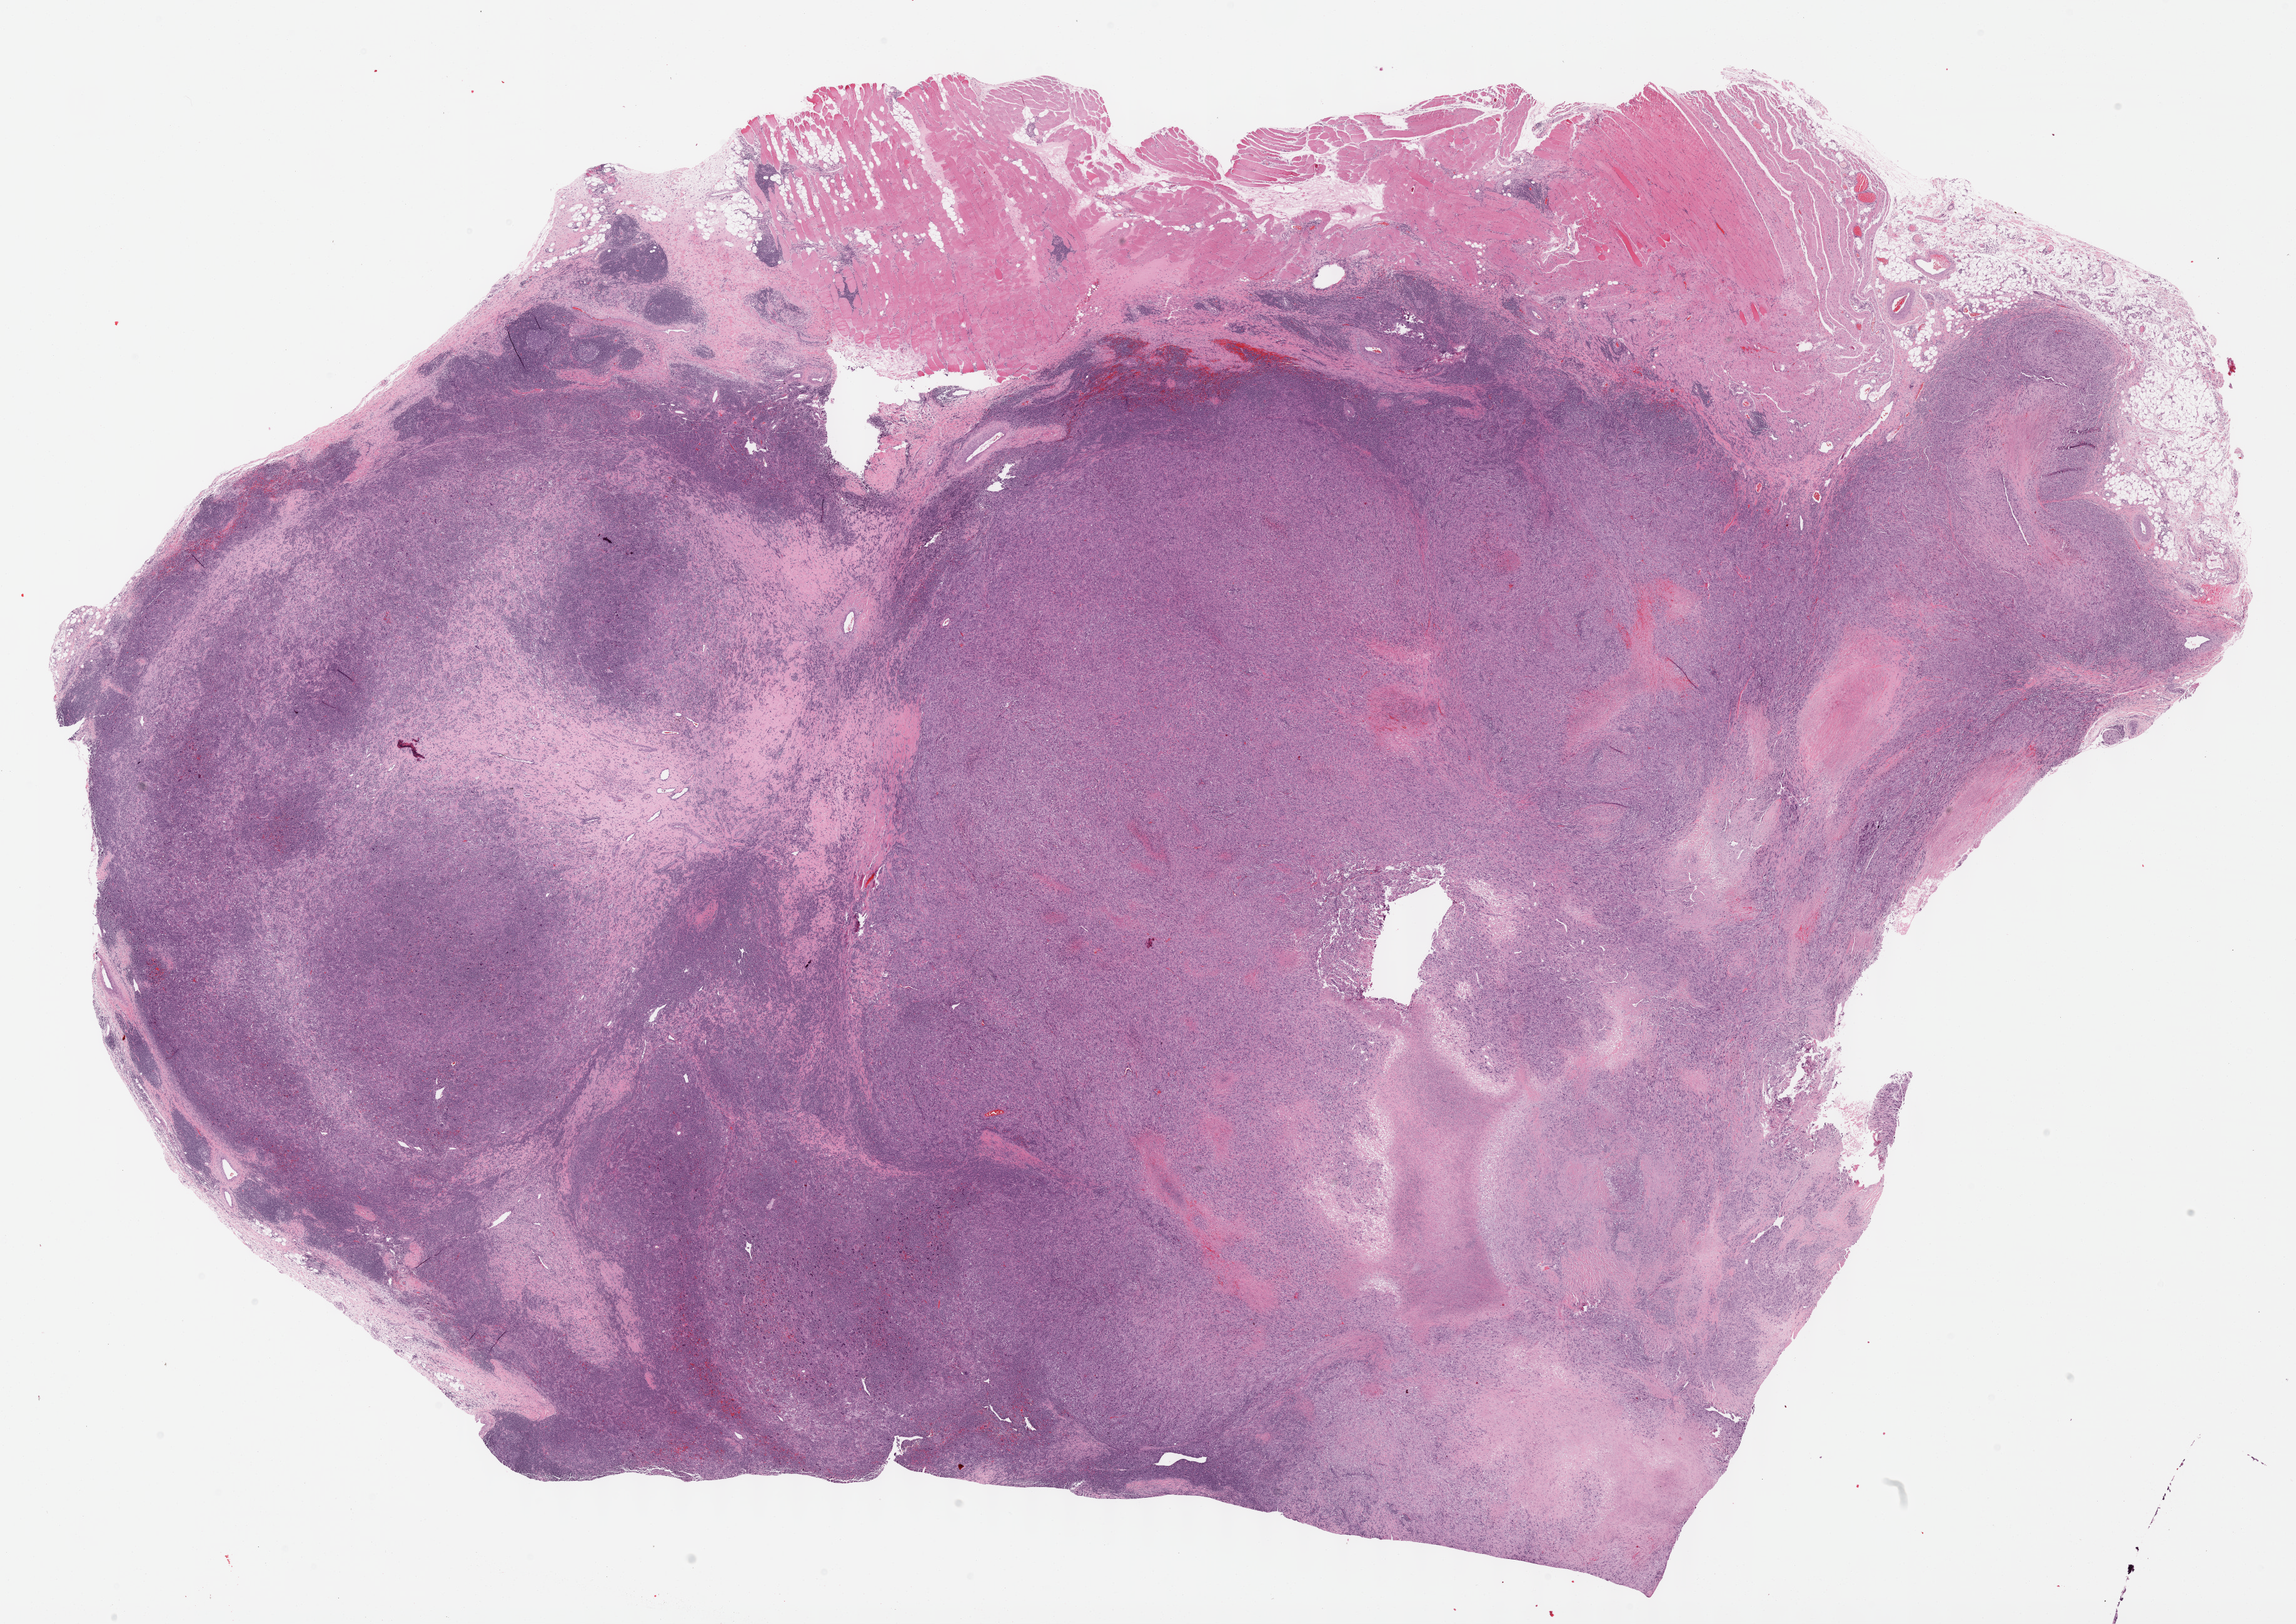
H&E whole-slide image, whole scanned area (about 29.7 x 21.0 mm, acquisition: 40x scan) shown as a low-resolution overview, formalin-fixed paraffin-embedded (FFPE) diagnostic section, primary tumour sample from the connective, subcutaneous and other soft tissues. Patient: male, age at initial diagnosis 59 years.
Pathologic diagnosis: Undifferentiated sarcoma.